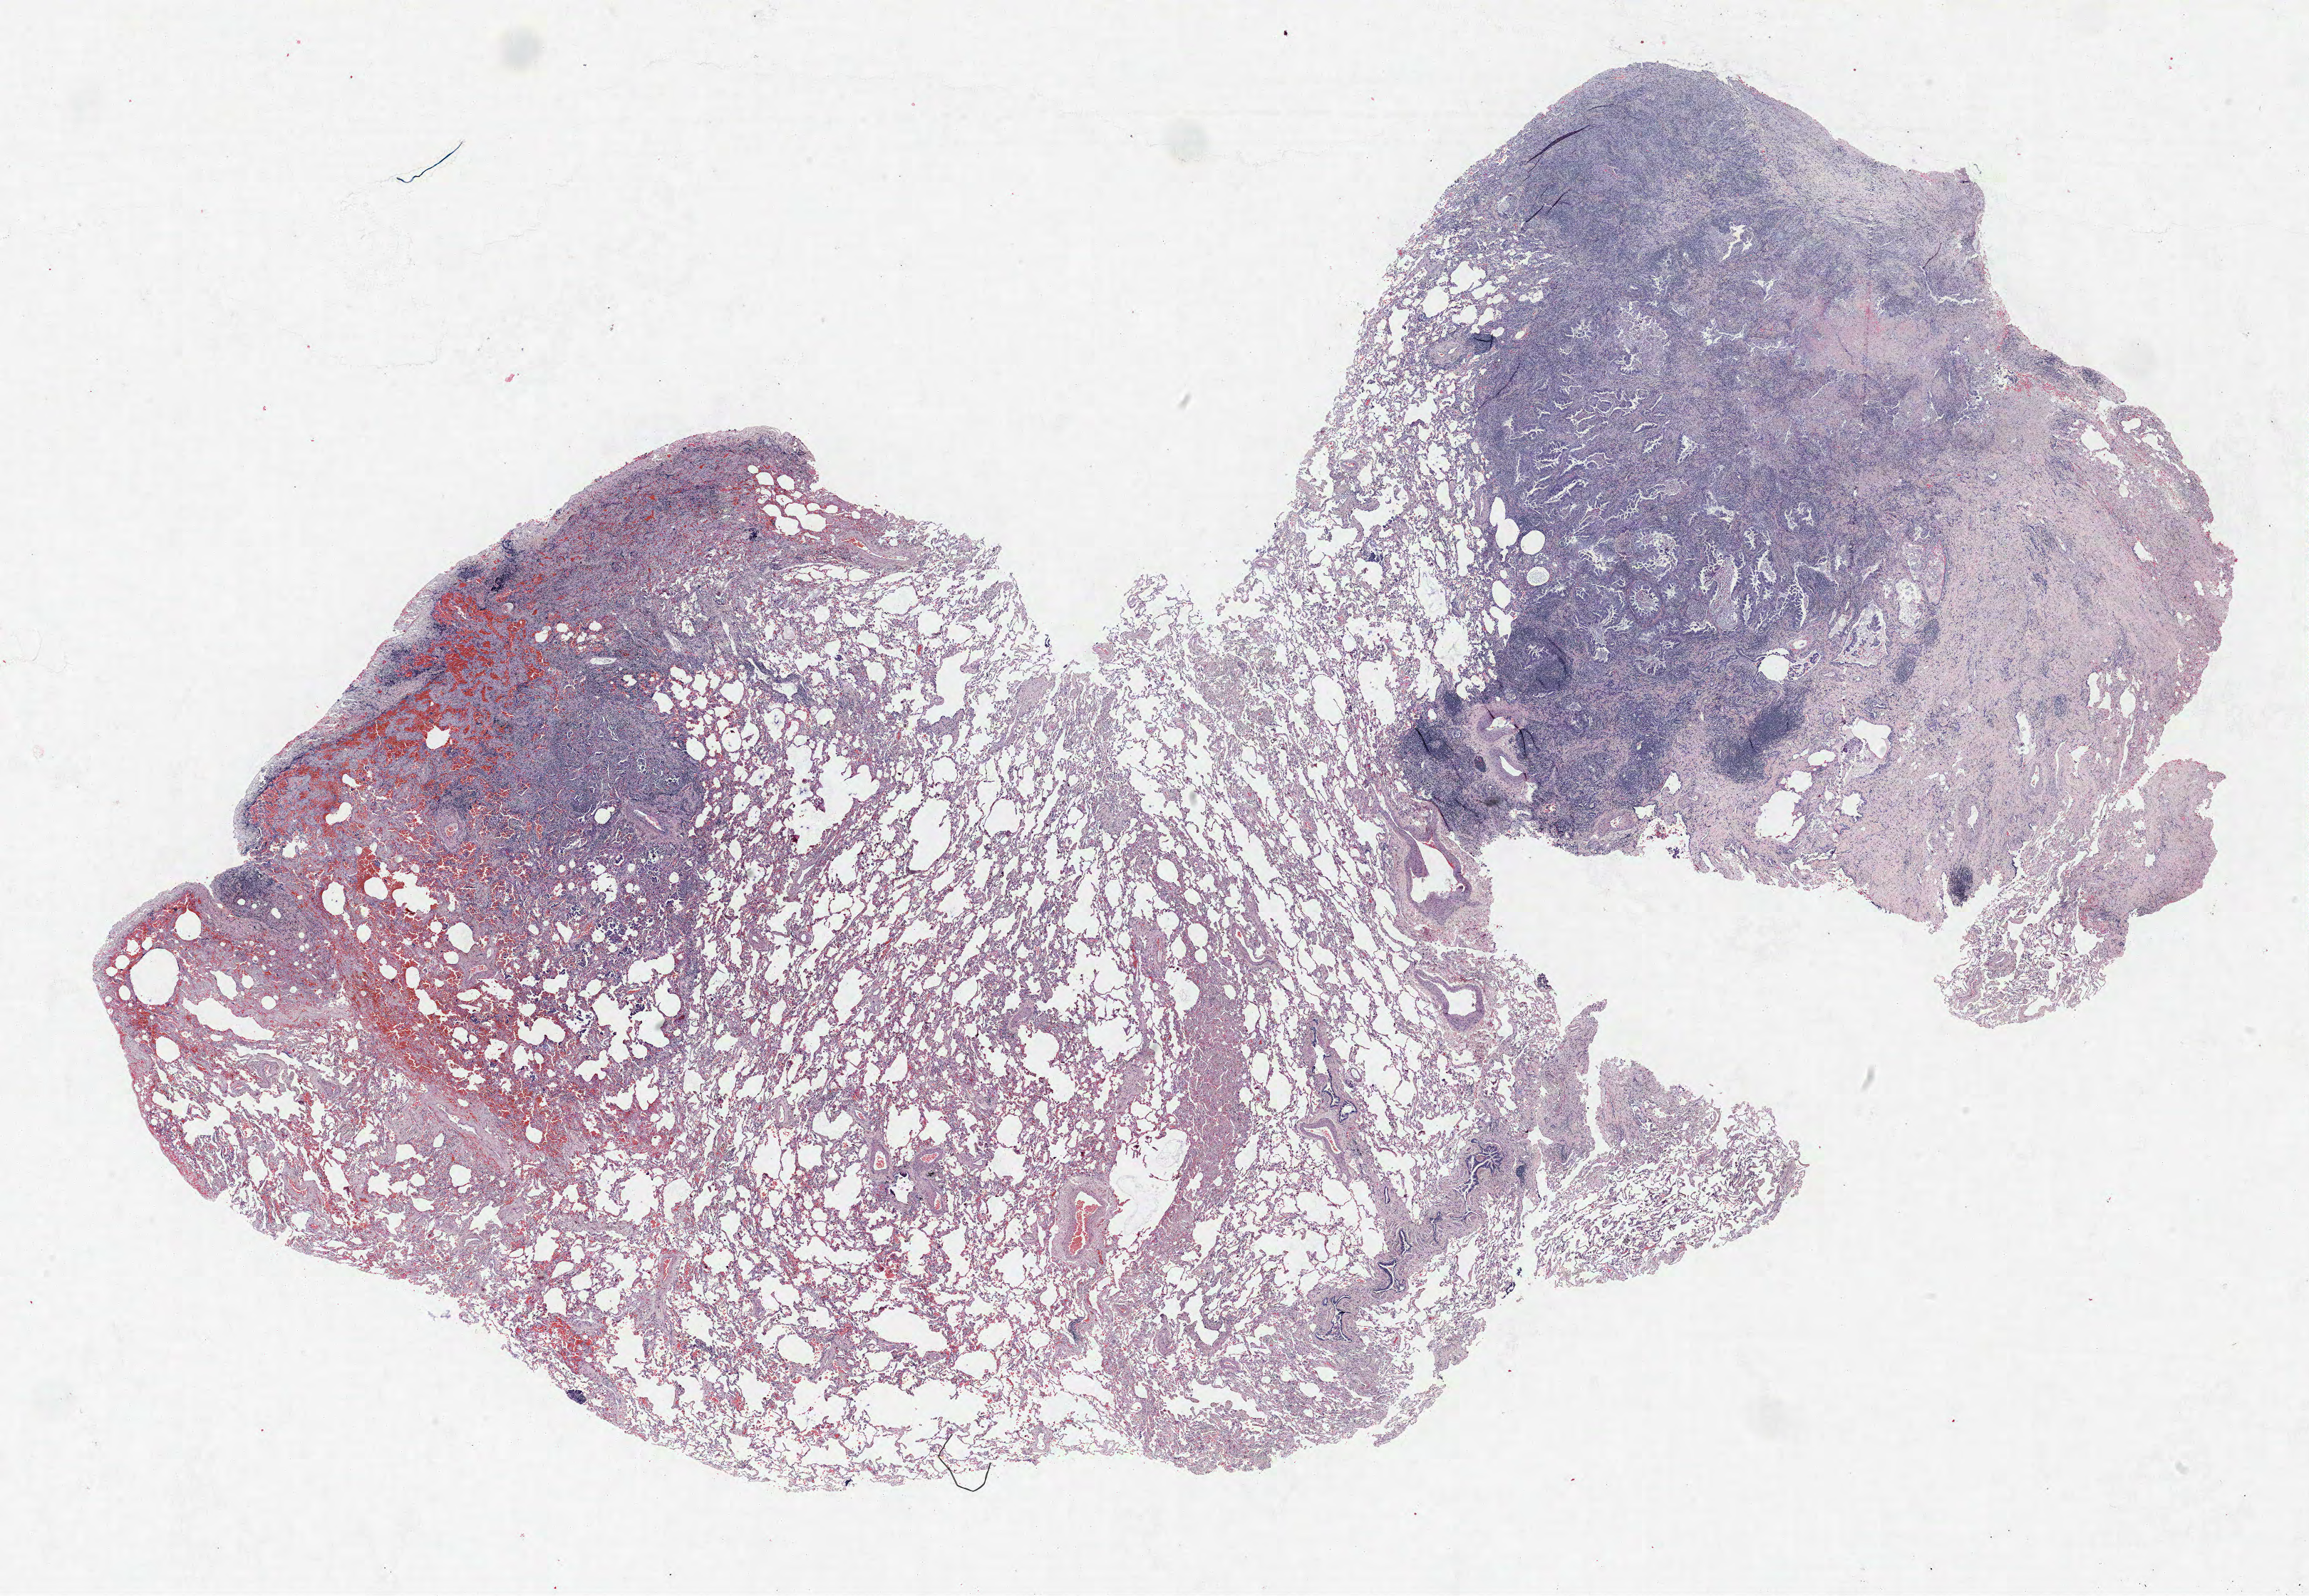
H&E-stained whole-slide image, whole scanned area (about 25.9 x 17.9 mm) shown as a low-resolution overview; formalin-fixed paraffin-embedded (FFPE) section; lung tissue. Female, age 56 at enrolment. Current smoker at enrolment. Grade: moderately differentiated (G2).
Stage (AJCC 6th edition): IA. Primary tumour location (clinical record): left upper lobe. Tumour size (pathology): 10 mm. Participant's lung-cancer diagnosis: Adenocarcinoma, NOS (ICD-O-3 8140/3).